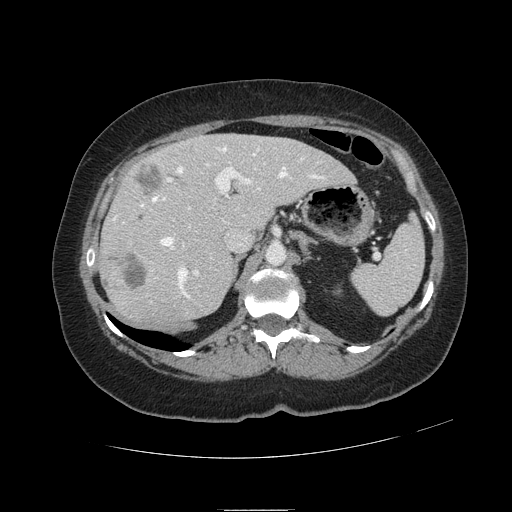
Contrast-enhanced abdominal CT, one axial slice. Slice 71 of 121 in the series (ordered by position). 120 kVp. Intravenous contrast given. Soft-tissue window (W 400 / L 40 HU). 2.5 mm slice thickness. 512 × 512 image matrix, field of view 400 × 400 mm. Female patient, age 52 years. Case-level facts recorded for this patient, not image findings: diagnosis: colorectal cancer liver metastases, imaged before liver resection; multiple liver metastases: yes; largest metastasis: 6.3 cm; disease in both lobes: no.
Outlined on this slice (manually delineated by an expert):
- hepatic veins: bounding box [x1, y1, x2, y2] px = [114, 148, 324, 298]
- liver: [101, 135, 353, 323]
- planned liver remnant (the part of the liver to remain after resection): [167, 134, 353, 228]
- portal vein (with intrahepatic branches): [123, 162, 266, 276]
- liver metastasis: [135, 165, 163, 196]
- liver metastasis: [125, 256, 147, 289]